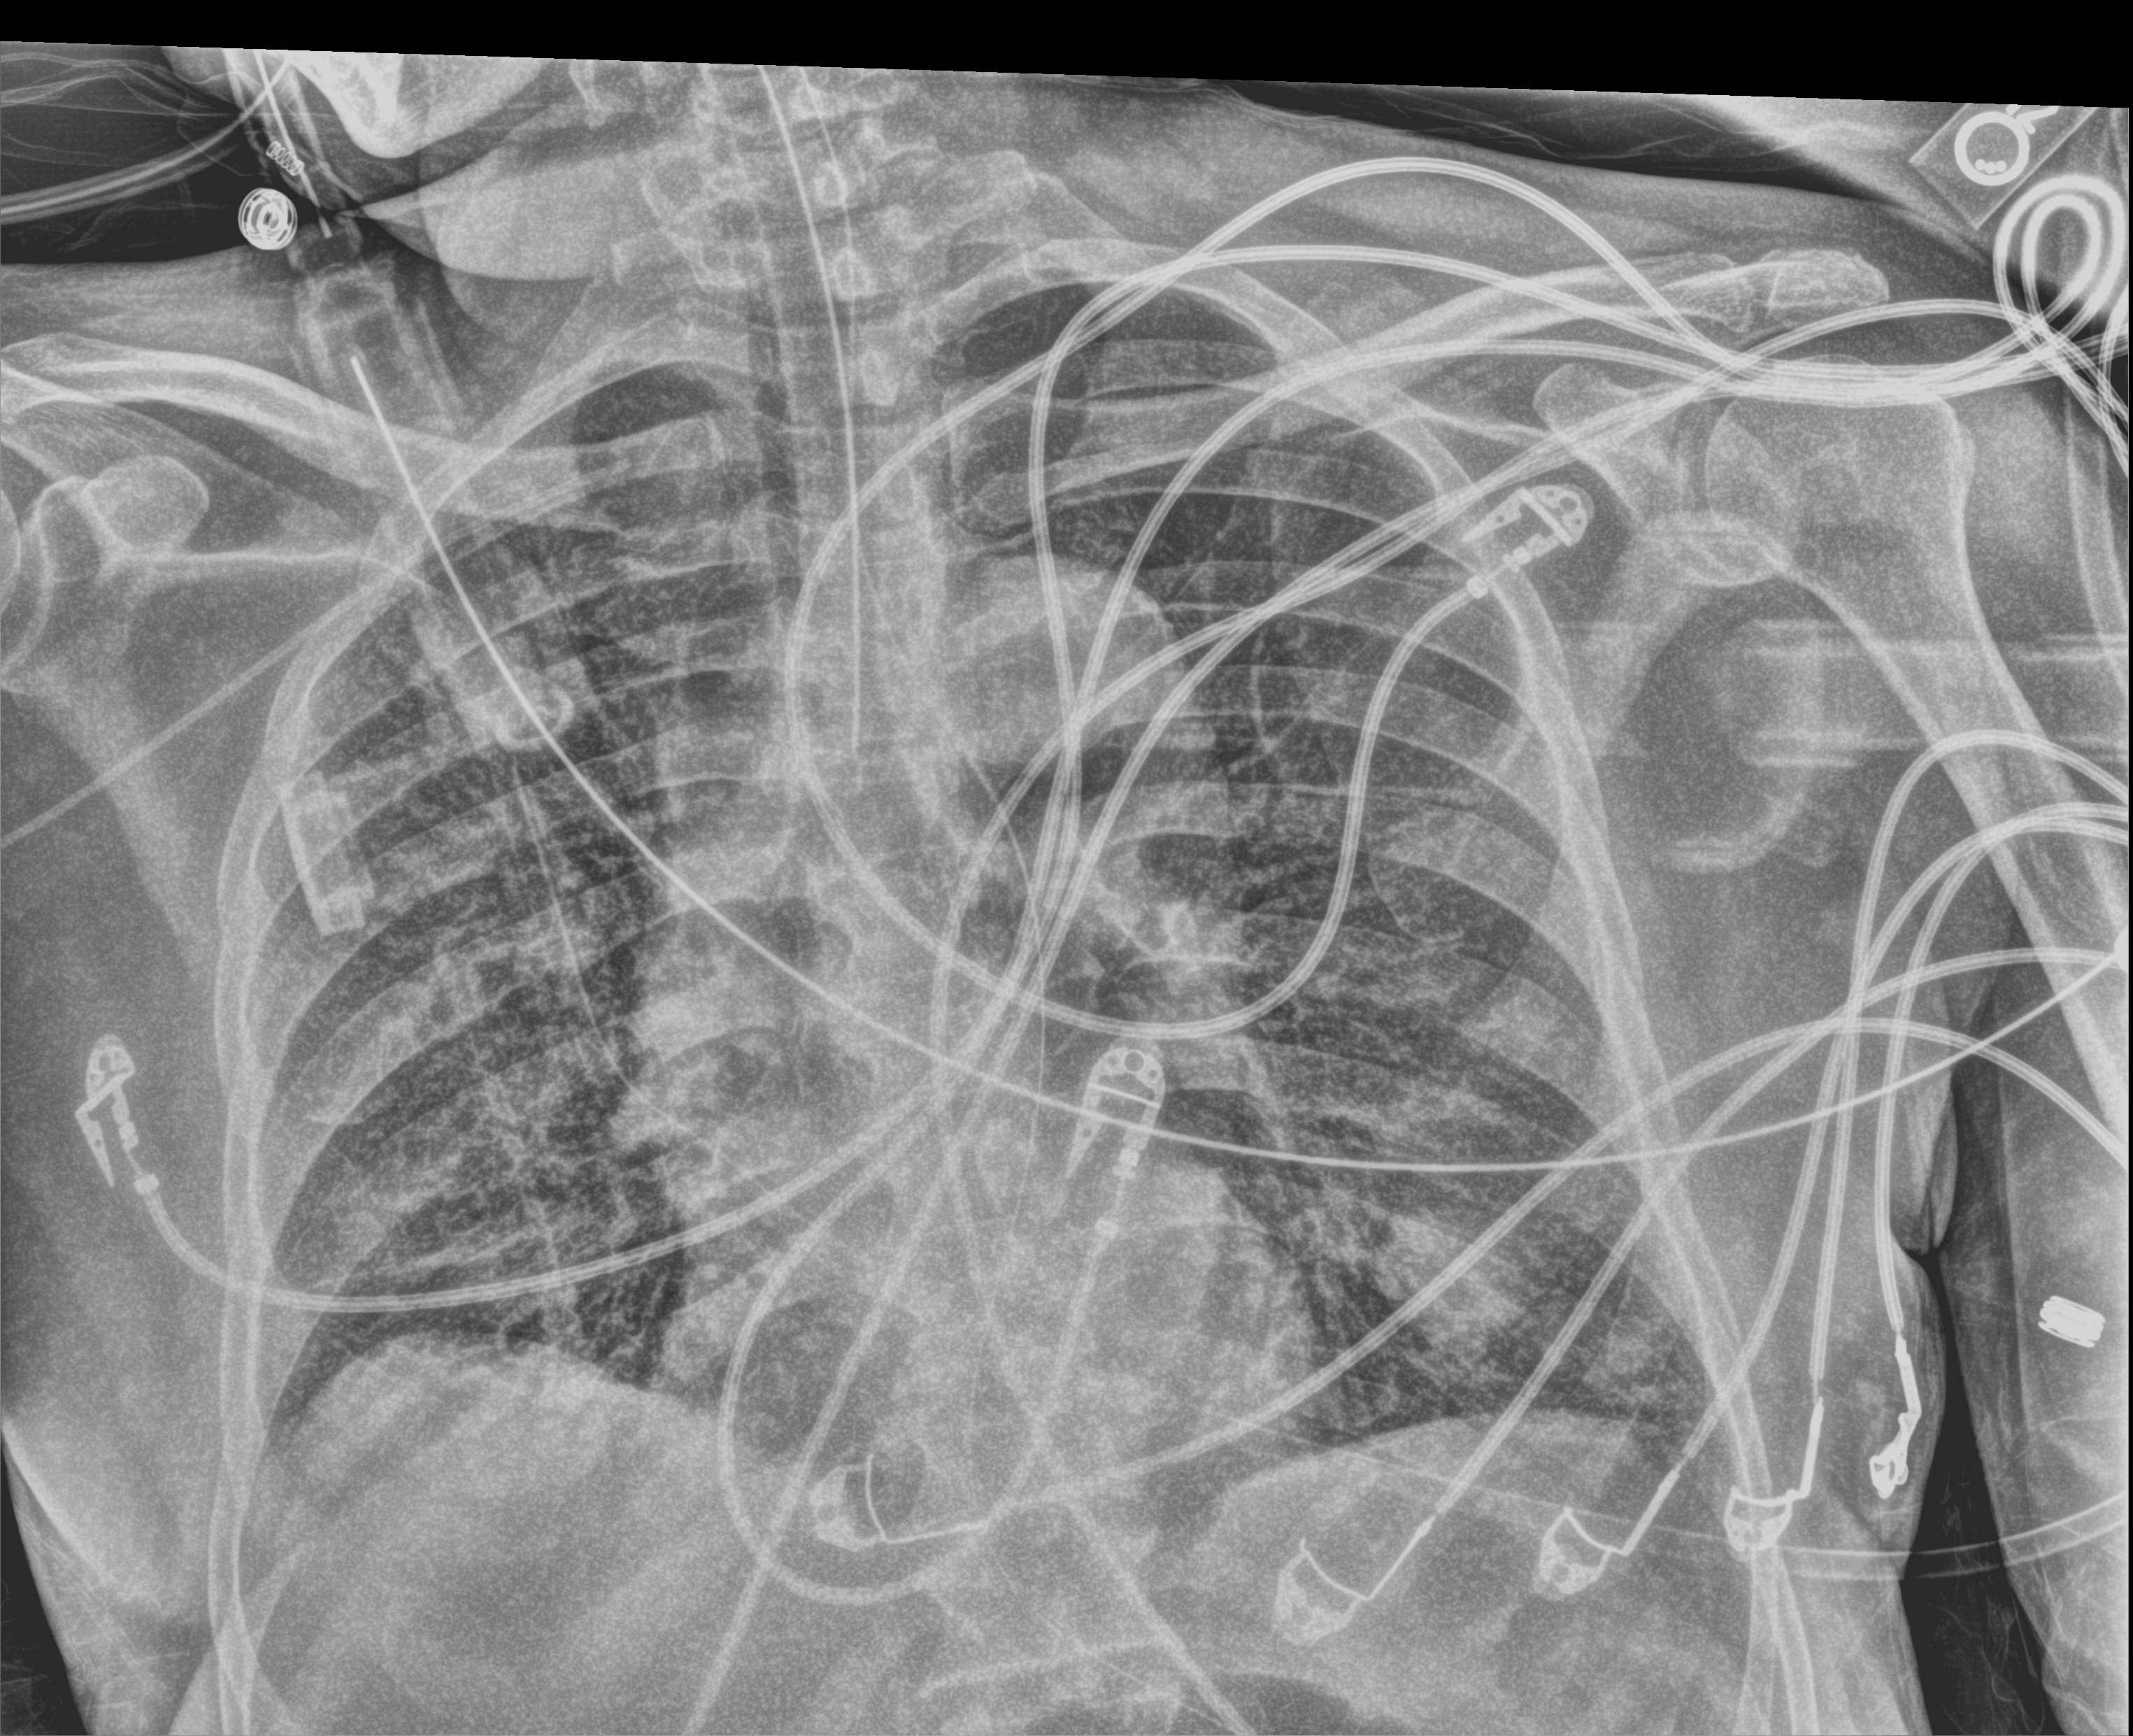
Chest X-ray (portable), anteroposterior (AP) projection. Patient hospitalised with COVID-19; male, aged 60–74 years.
Admission-level facts for this patient (not findings on this image; timing relative to this image not recorded):
- length of hospital stay: 10 days
- mechanically ventilated during this hospital stay: yes